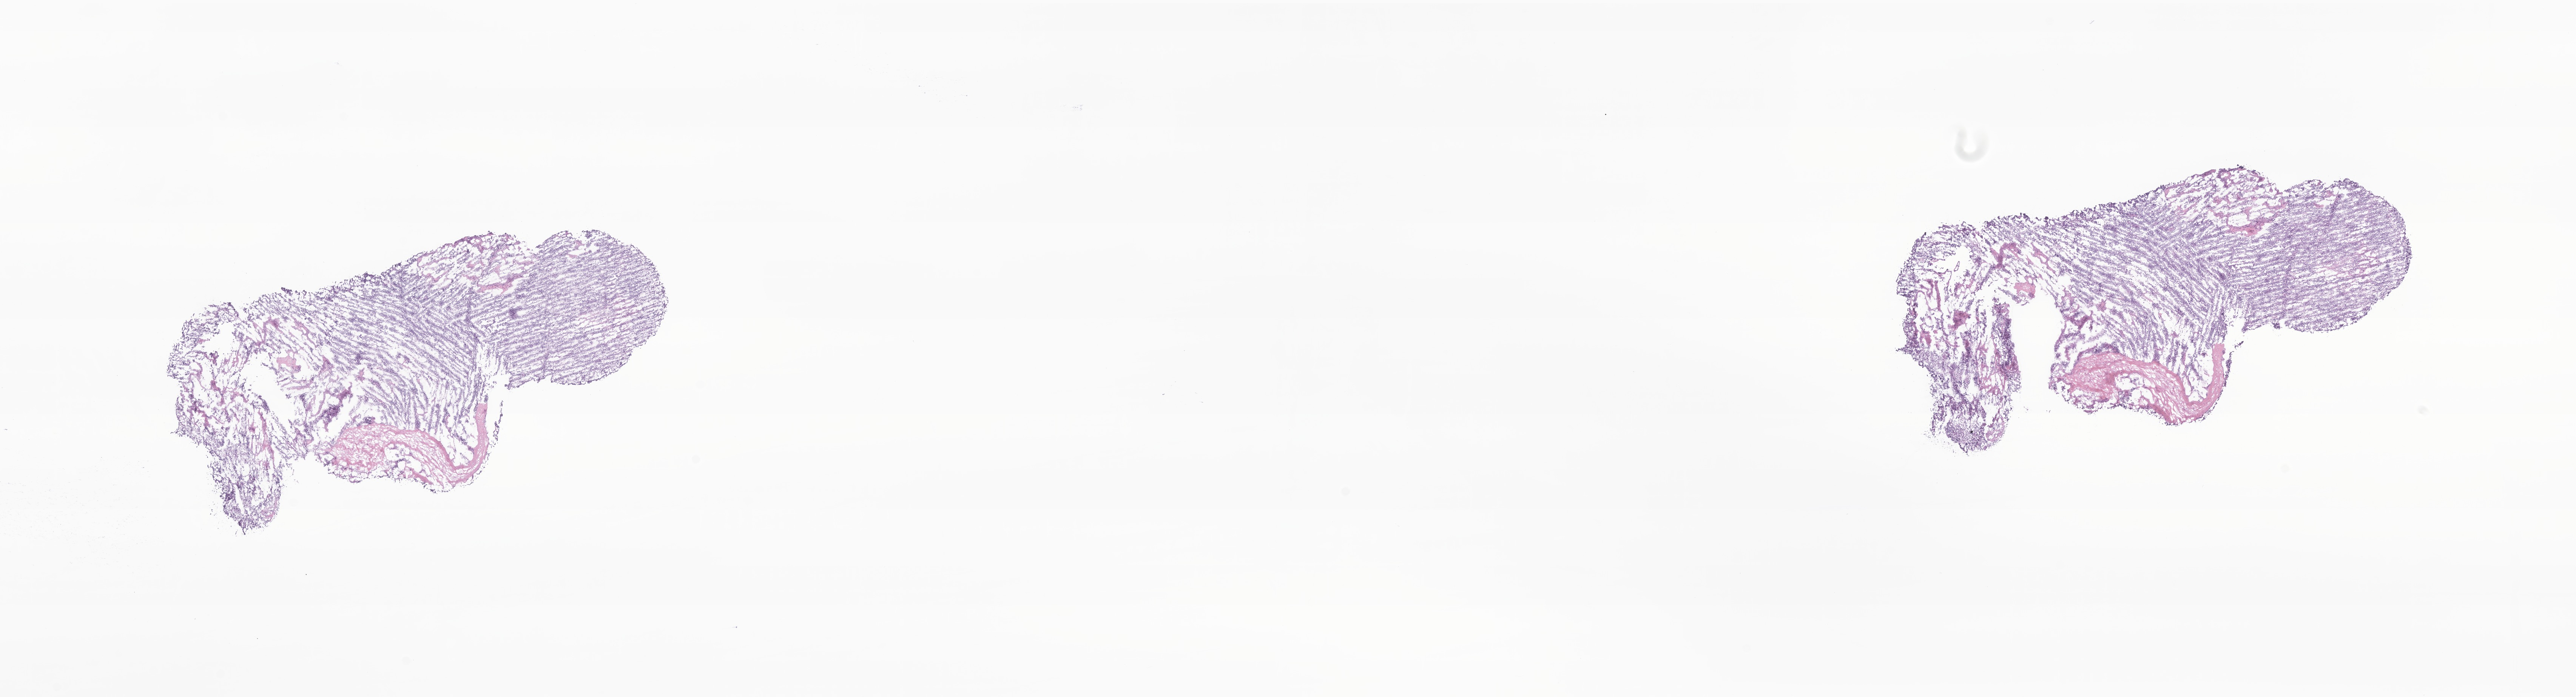
Digitized hematoxylin and eosin (H&E)-stained section of tumor tissue from the retroperitoneum — low-resolution overview of the scanned area, about 28.8 x 7.8 mm. Frozen section (OCT-embedded). Male patient, age 877 days.
* diagnosis (ICD-O-3 morphology term): Neuroblastoma, NOS